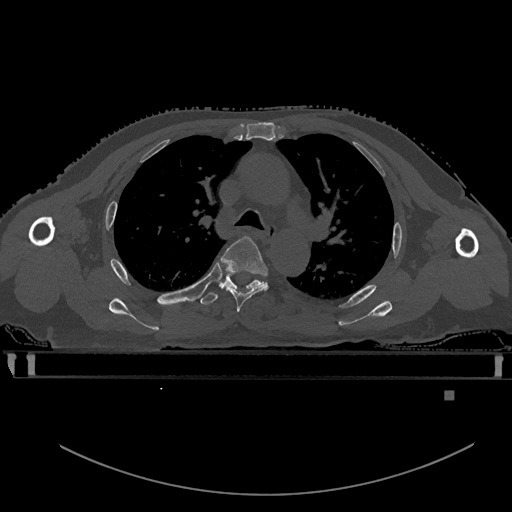
CT including the spine, one axial slice. Slice 388 of 969 in the series (ordered by position). Bone window (W 1800 / L 400 HU). 0.5 mm slice thickness. 512 × 512 image matrix, field of view 456 × 456 mm. Patient: male, 82 years. From the clinical record (not read from this slice): primary cancer: prostate; vertebrae with lytic lesions (as recorded): T11, T9, T8, T2.
Annotated regions visible in this slice (semi-automatic segmentation, software-assisted and operator-edited):
- T4 vertebra: bounding box (x1, y1, x2, y2) in pixels: (220, 236, 268, 313)
- T5 vertebra: (200, 272, 263, 306)